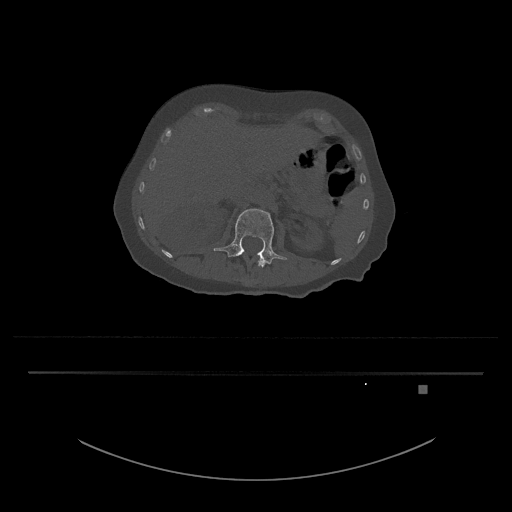
CT including the spine, one axial slice. Slice 504 of 797 in the series (ordered by position). Reconstruction kernel Br40s/3. 120 kVp. Bone window (W 1800 / L 400 HU). 0.5 mm slice thickness. 512 × 512 image matrix, field of view 500 × 500 mm. Female patient, age 57 years. Case-level facts recorded for this patient, not image findings: primary cancer: cervical.
Structures marked on this image (semi-automatic segmentation, software-assisted and operator-edited):
- L1 vertebra: bounding box <244,250,265,267> (left, top, right, bottom; pixels)